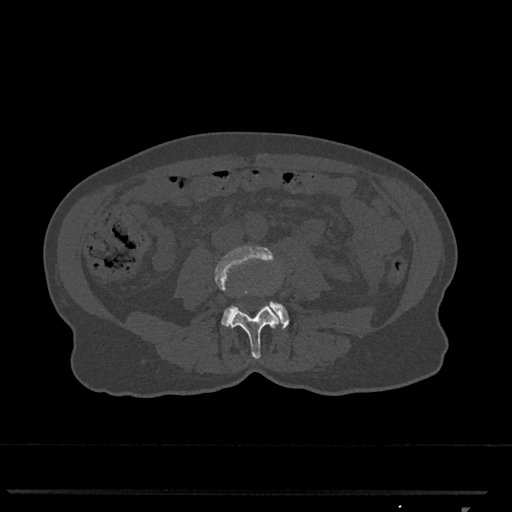
CT including the spine, one axial slice. Slice 247 of 793 in the series (ordered by position). Bone window (W 1800 / L 400 HU). 0.5 mm slice thickness. 512 × 512 image matrix, field of view 380 × 380 mm. Patient: female, 62 years. From the clinical record (not read from this slice): primary cancer: renal.
Structures marked on this image (semi-automatically segmented with operator editing):
- L3 vertebra: bounding box (x1, y1, x2, y2) in pixels: (215, 246, 283, 359)
- L4 vertebra: (222, 301, 289, 329)